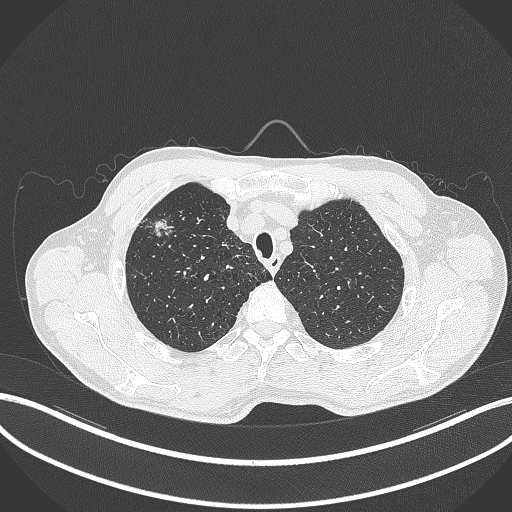
Chest CT, one axial slice. Slice 352 of 427 in the series (ordered by position). Reconstruction kernel B70f. Lung window (W 1500 / L -600 HU). 512 × 512 image matrix, field of view 400 × 400 mm. Male patient, age 69 years. Case-level facts recorded for this patient, not image findings: clinical TNM (as recorded): T1b N1 M0.
Structures marked on this image (bounding box drawn by a radiologist):
- lung tumour (recorded histology: adenocarcinoma): bounding box [x1, y1, x2, y2] px = [148, 214, 176, 243]